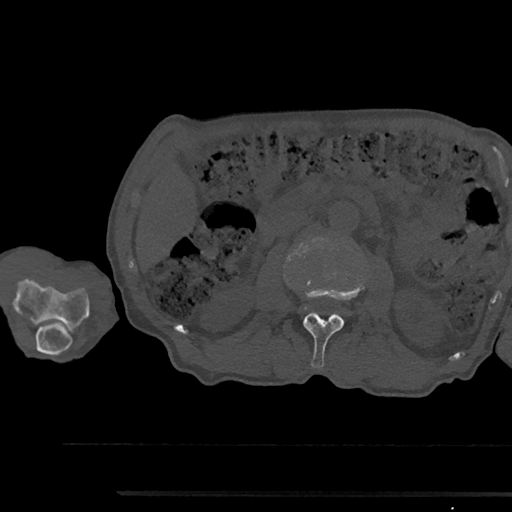
CT including the spine, one axial slice; position 542 of 797 along the scan axis; reconstruction kernel Br40s/3; bone window (W 1800 / L 400 HU); 0.5 mm slice thickness; 512 × 512 image matrix. Male patient, age 79 years. From the clinical record (not read from this slice): primary cancer: prostate.
Structures marked on this image (semi-automatically segmented with operator editing):
- L2 vertebra: bounding box [x1, y1, x2, y2] px = [303, 280, 364, 368]